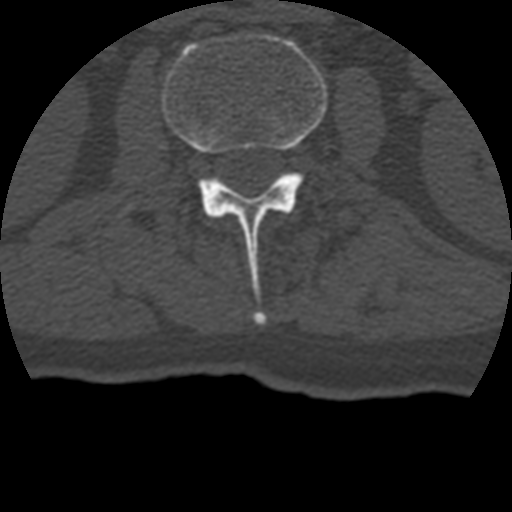
CT including the spine, one axial slice; position 115 of 399 along the scan axis; bone window (W 1800 / L 400 HU); 512 × 512 image matrix, field of view 160 × 160 mm. Patient age 69 years. From the clinical record (not read from this slice): primary cancer: prostate.
Annotated regions visible in this slice (semi-automatic segmentation, software-assisted and operator-edited):
- L2 vertebra: bounding box <162,33,327,324> (left, top, right, bottom; pixels)